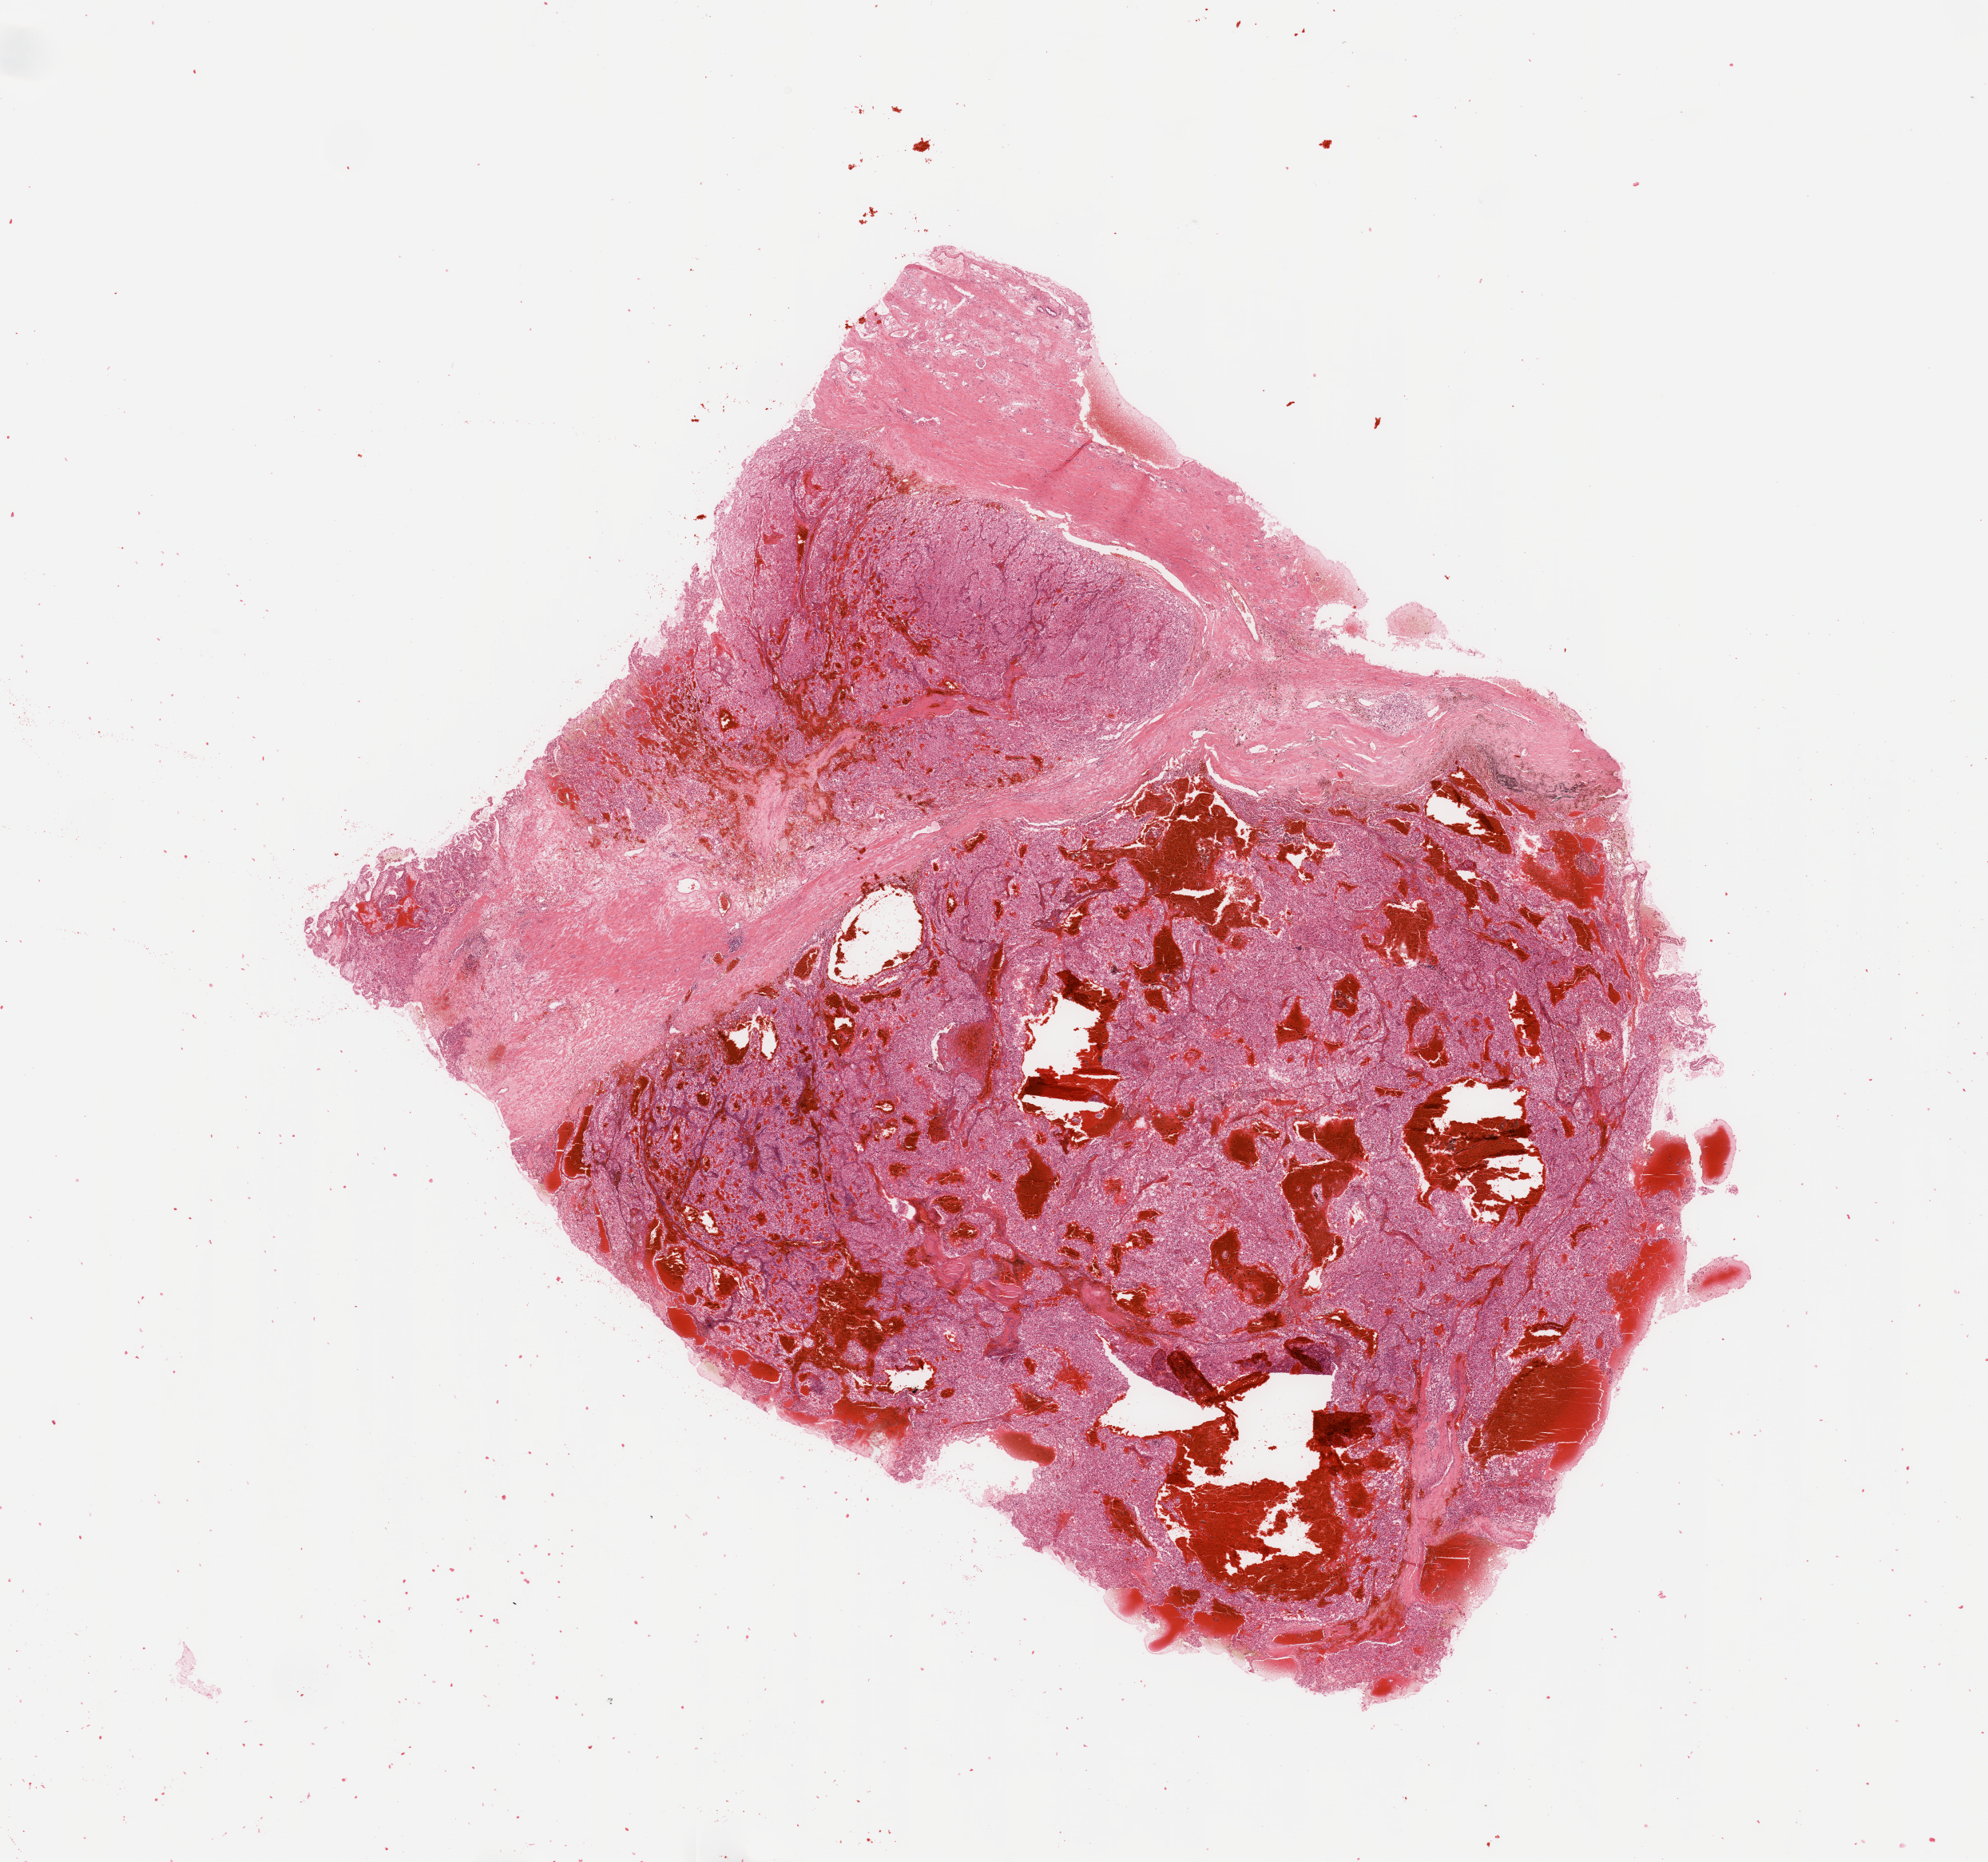
Whole-slide histology image, Hematoxylin and eosin (H&E) stained — whole scanned area (about 19.7 x 18.4 mm) shown as a low-resolution overview, tumour tissue sample, sampled site: kidney. Male, 52 y/o. Histologic grade: G2 (moderately differentiated). Slide review estimates, as recorded: tumour nuclei 85%, necrosis 5%.
* diagnosis: Renal cell carcinoma, NOS
* AJCC pathologic stage: III